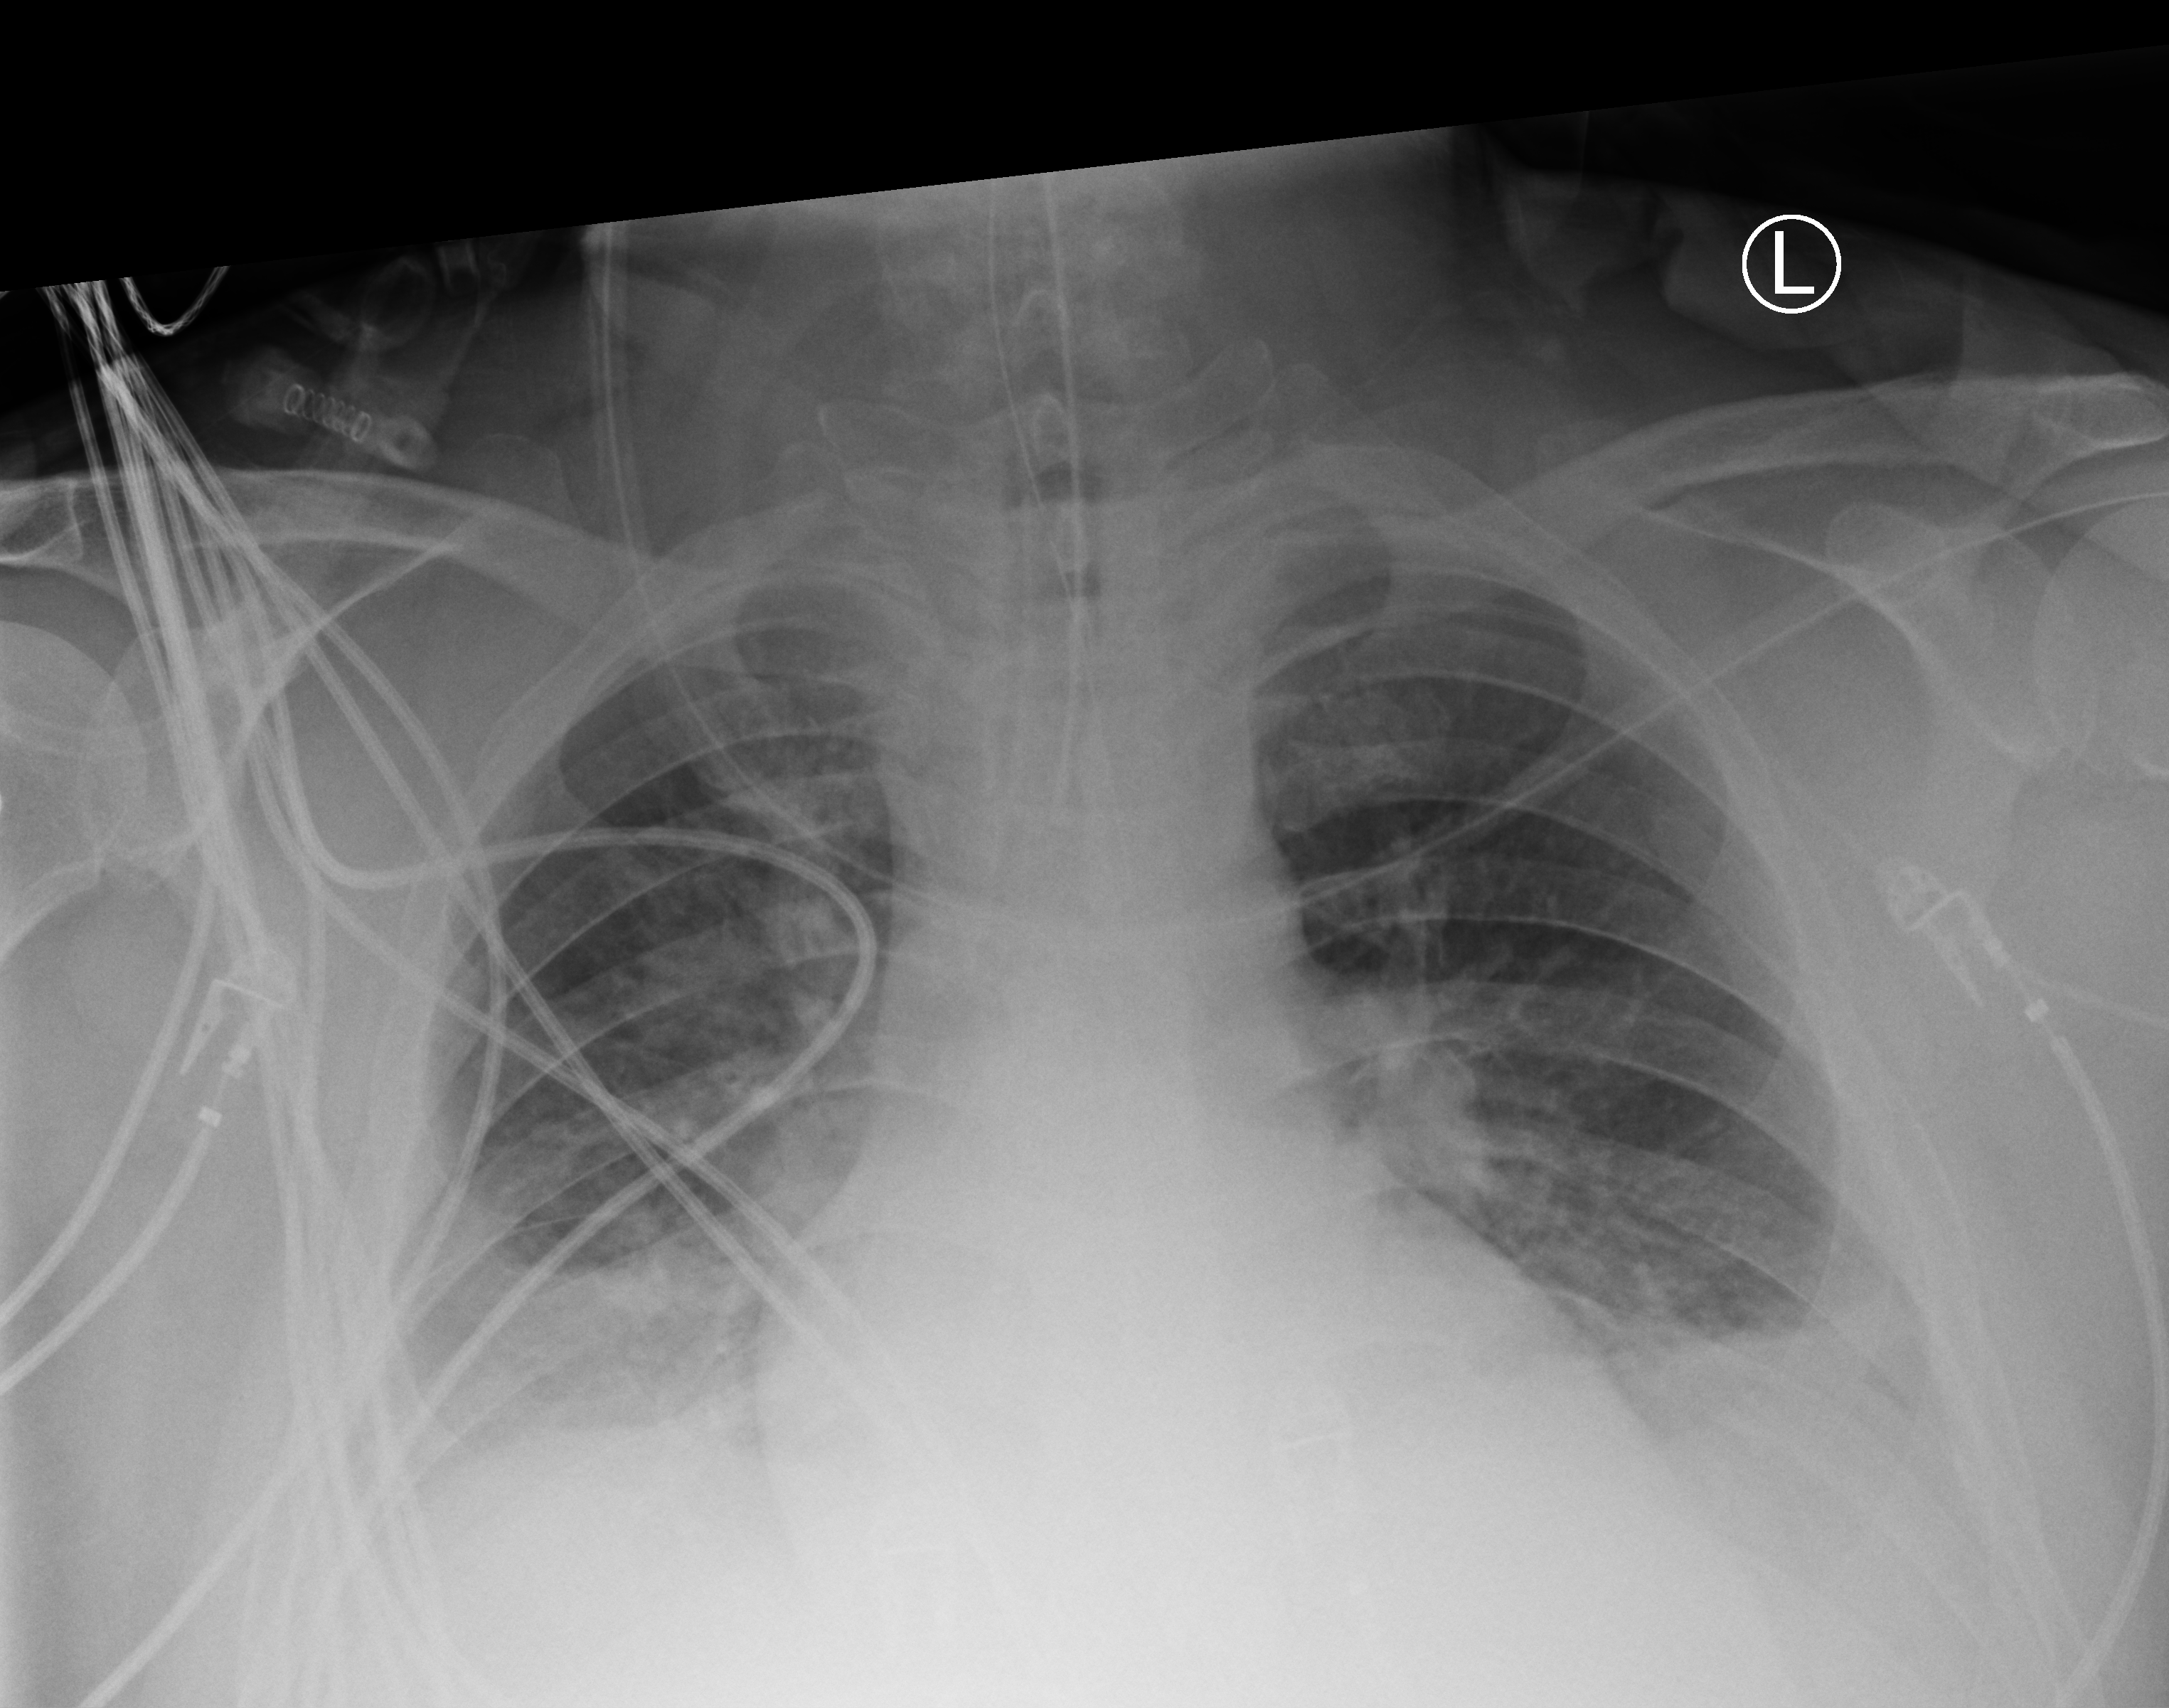
Chest X-ray (portable), anteroposterior (AP) projection. Male patient hospitalised with COVID-19, age 18–59 years.
From the hospital-stay record, not from the radiograph (when in the stay this image was taken is not recorded):
- admitted to intensive care during this hospital stay: yes
- length of hospital stay: 65 days
- mechanically ventilated during this hospital stay: yes